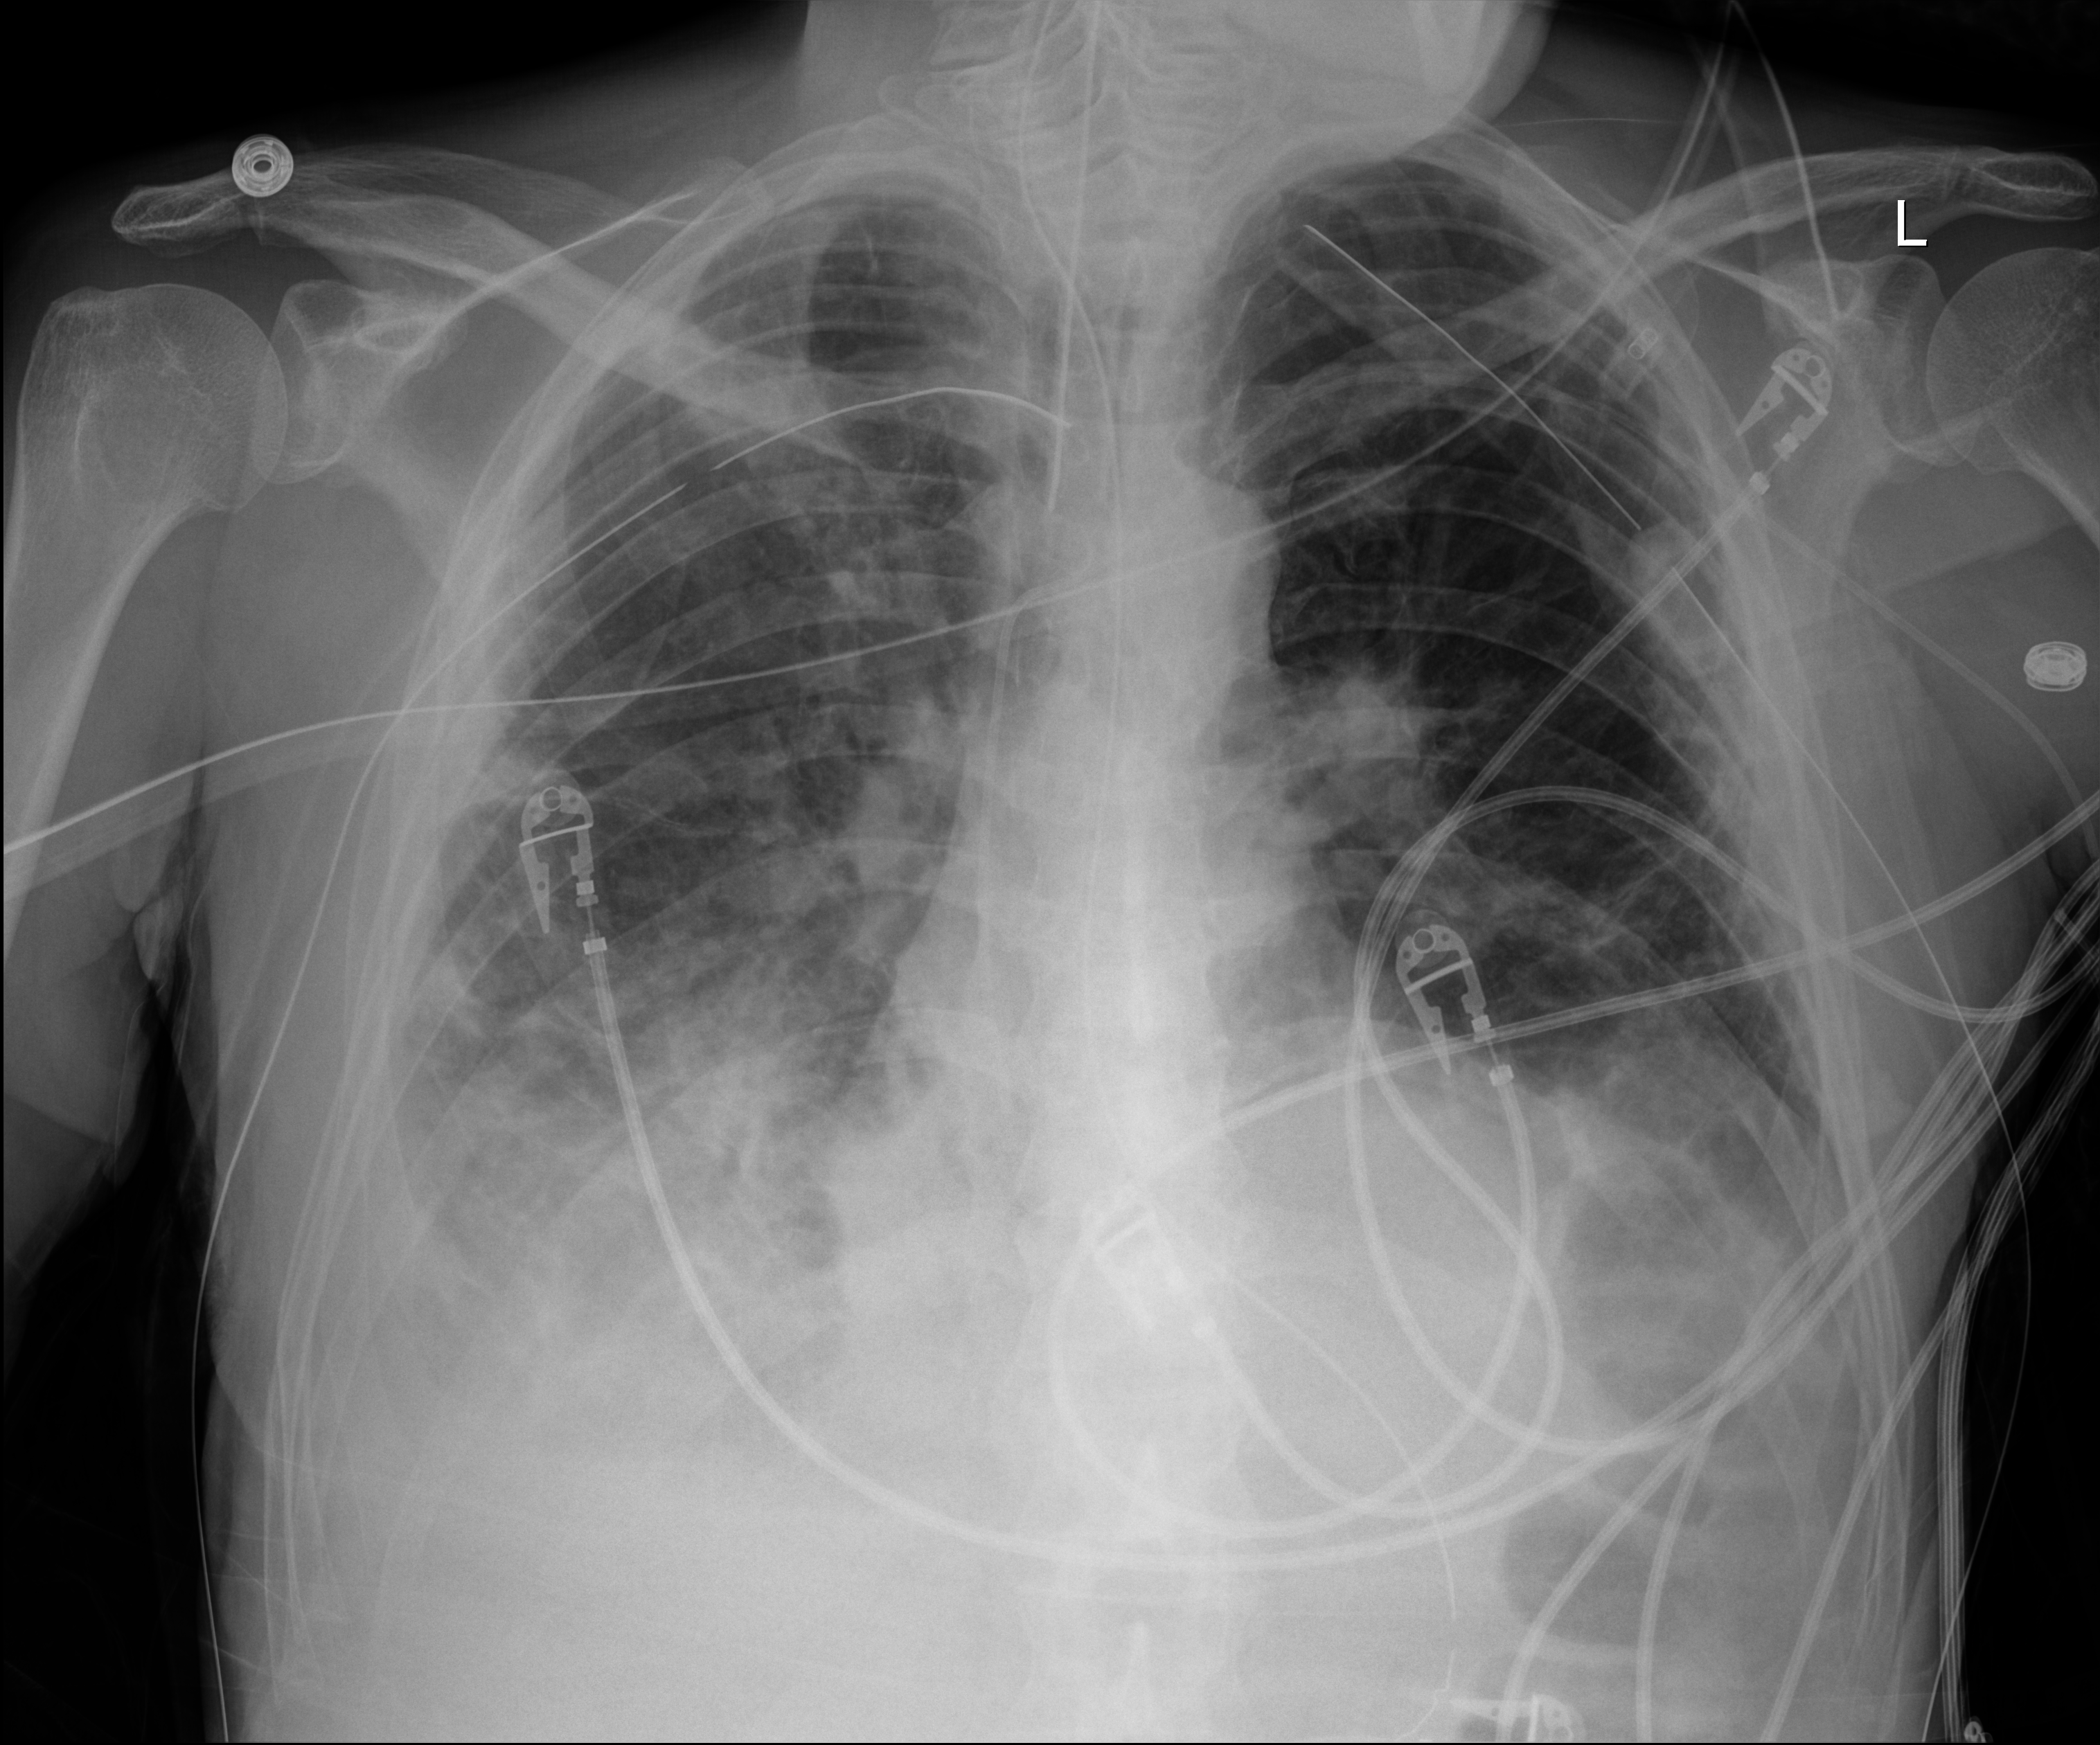
Chest radiograph (digital radiography). Male patient hospitalised with COVID-19, age 18–59 years.
From the hospital-stay record, not from the radiograph (when in the stay this image was taken is not recorded): hypertension (admission record): yes; admitted to intensive care during this hospital stay: yes.